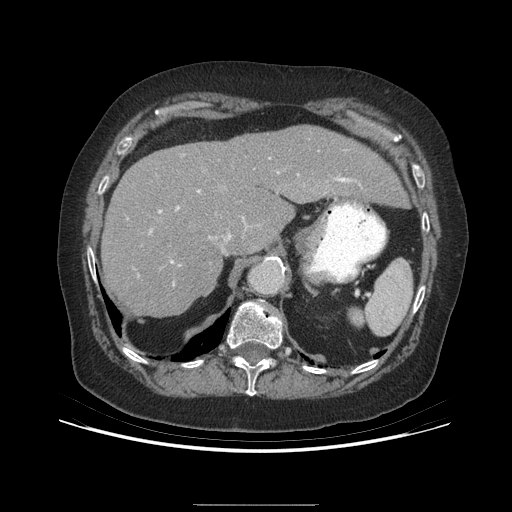
Contrast-enhanced abdominal CT (liver protocol), one axial slice. Slice 166 of 192 in the series (ordered by position). 140 kVp. Soft-tissue window (W 400 / L 40 HU). 2.5 mm slice thickness. 512 × 512 image matrix, field of view 400 × 400 mm. Case-level facts recorded for this patient, not image findings: diagnosis: hepatocellular carcinoma (patient treated with transarterial chemoembolisation; whether this scan precedes or follows treatment is not stated here); TNM stage (as recorded): Stage-I.
Structures marked on this image (semi-automatic segmentation, software-assisted and operator-edited):
- liver parenchyma outside the tumour (the mass and vessels are separate outlines, so this box may not span the whole liver): bounding box (x1, y1, x2, y2) in pixels: (100, 126, 406, 316)
- liver vessels: (159, 172, 350, 263)